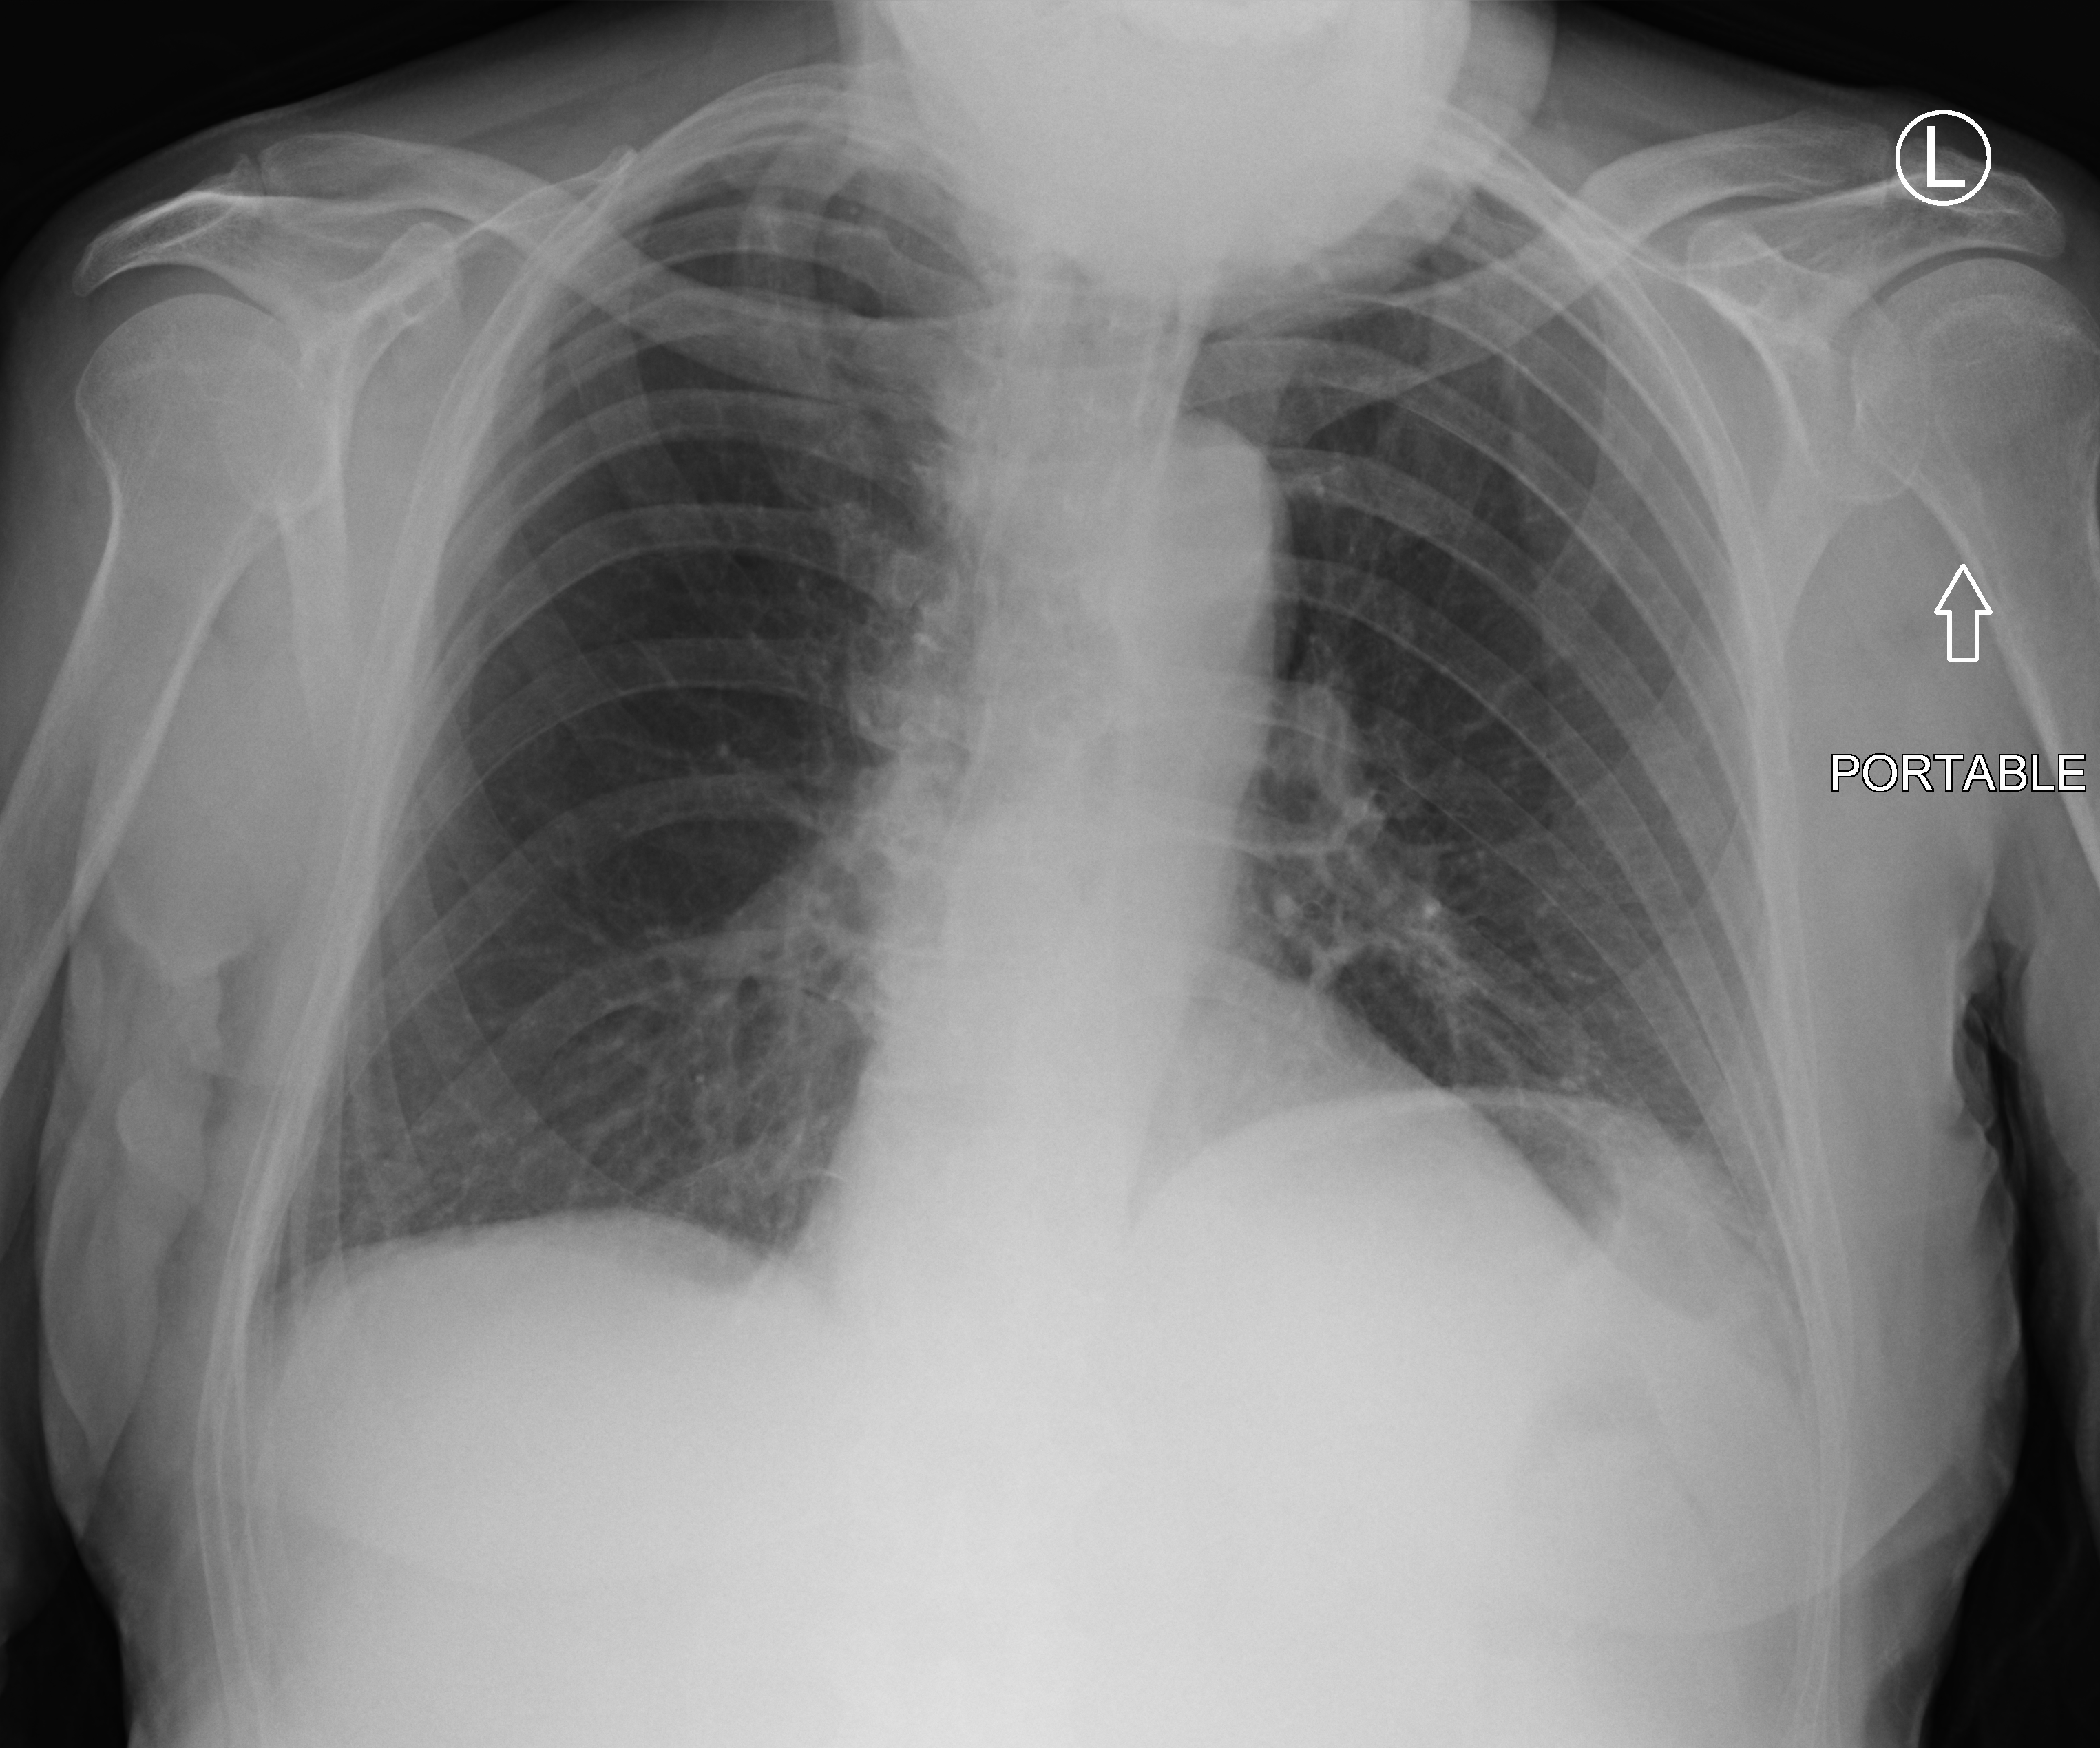
Portable chest radiograph; anteroposterior (AP) projection. Patient hospitalised with COVID-19; male, aged 75–90 years.
Admission-level facts for this patient (not findings on this image; timing relative to this image not recorded):
- admitted to intensive care during this hospital stay: no
- mechanically ventilated during this hospital stay: no